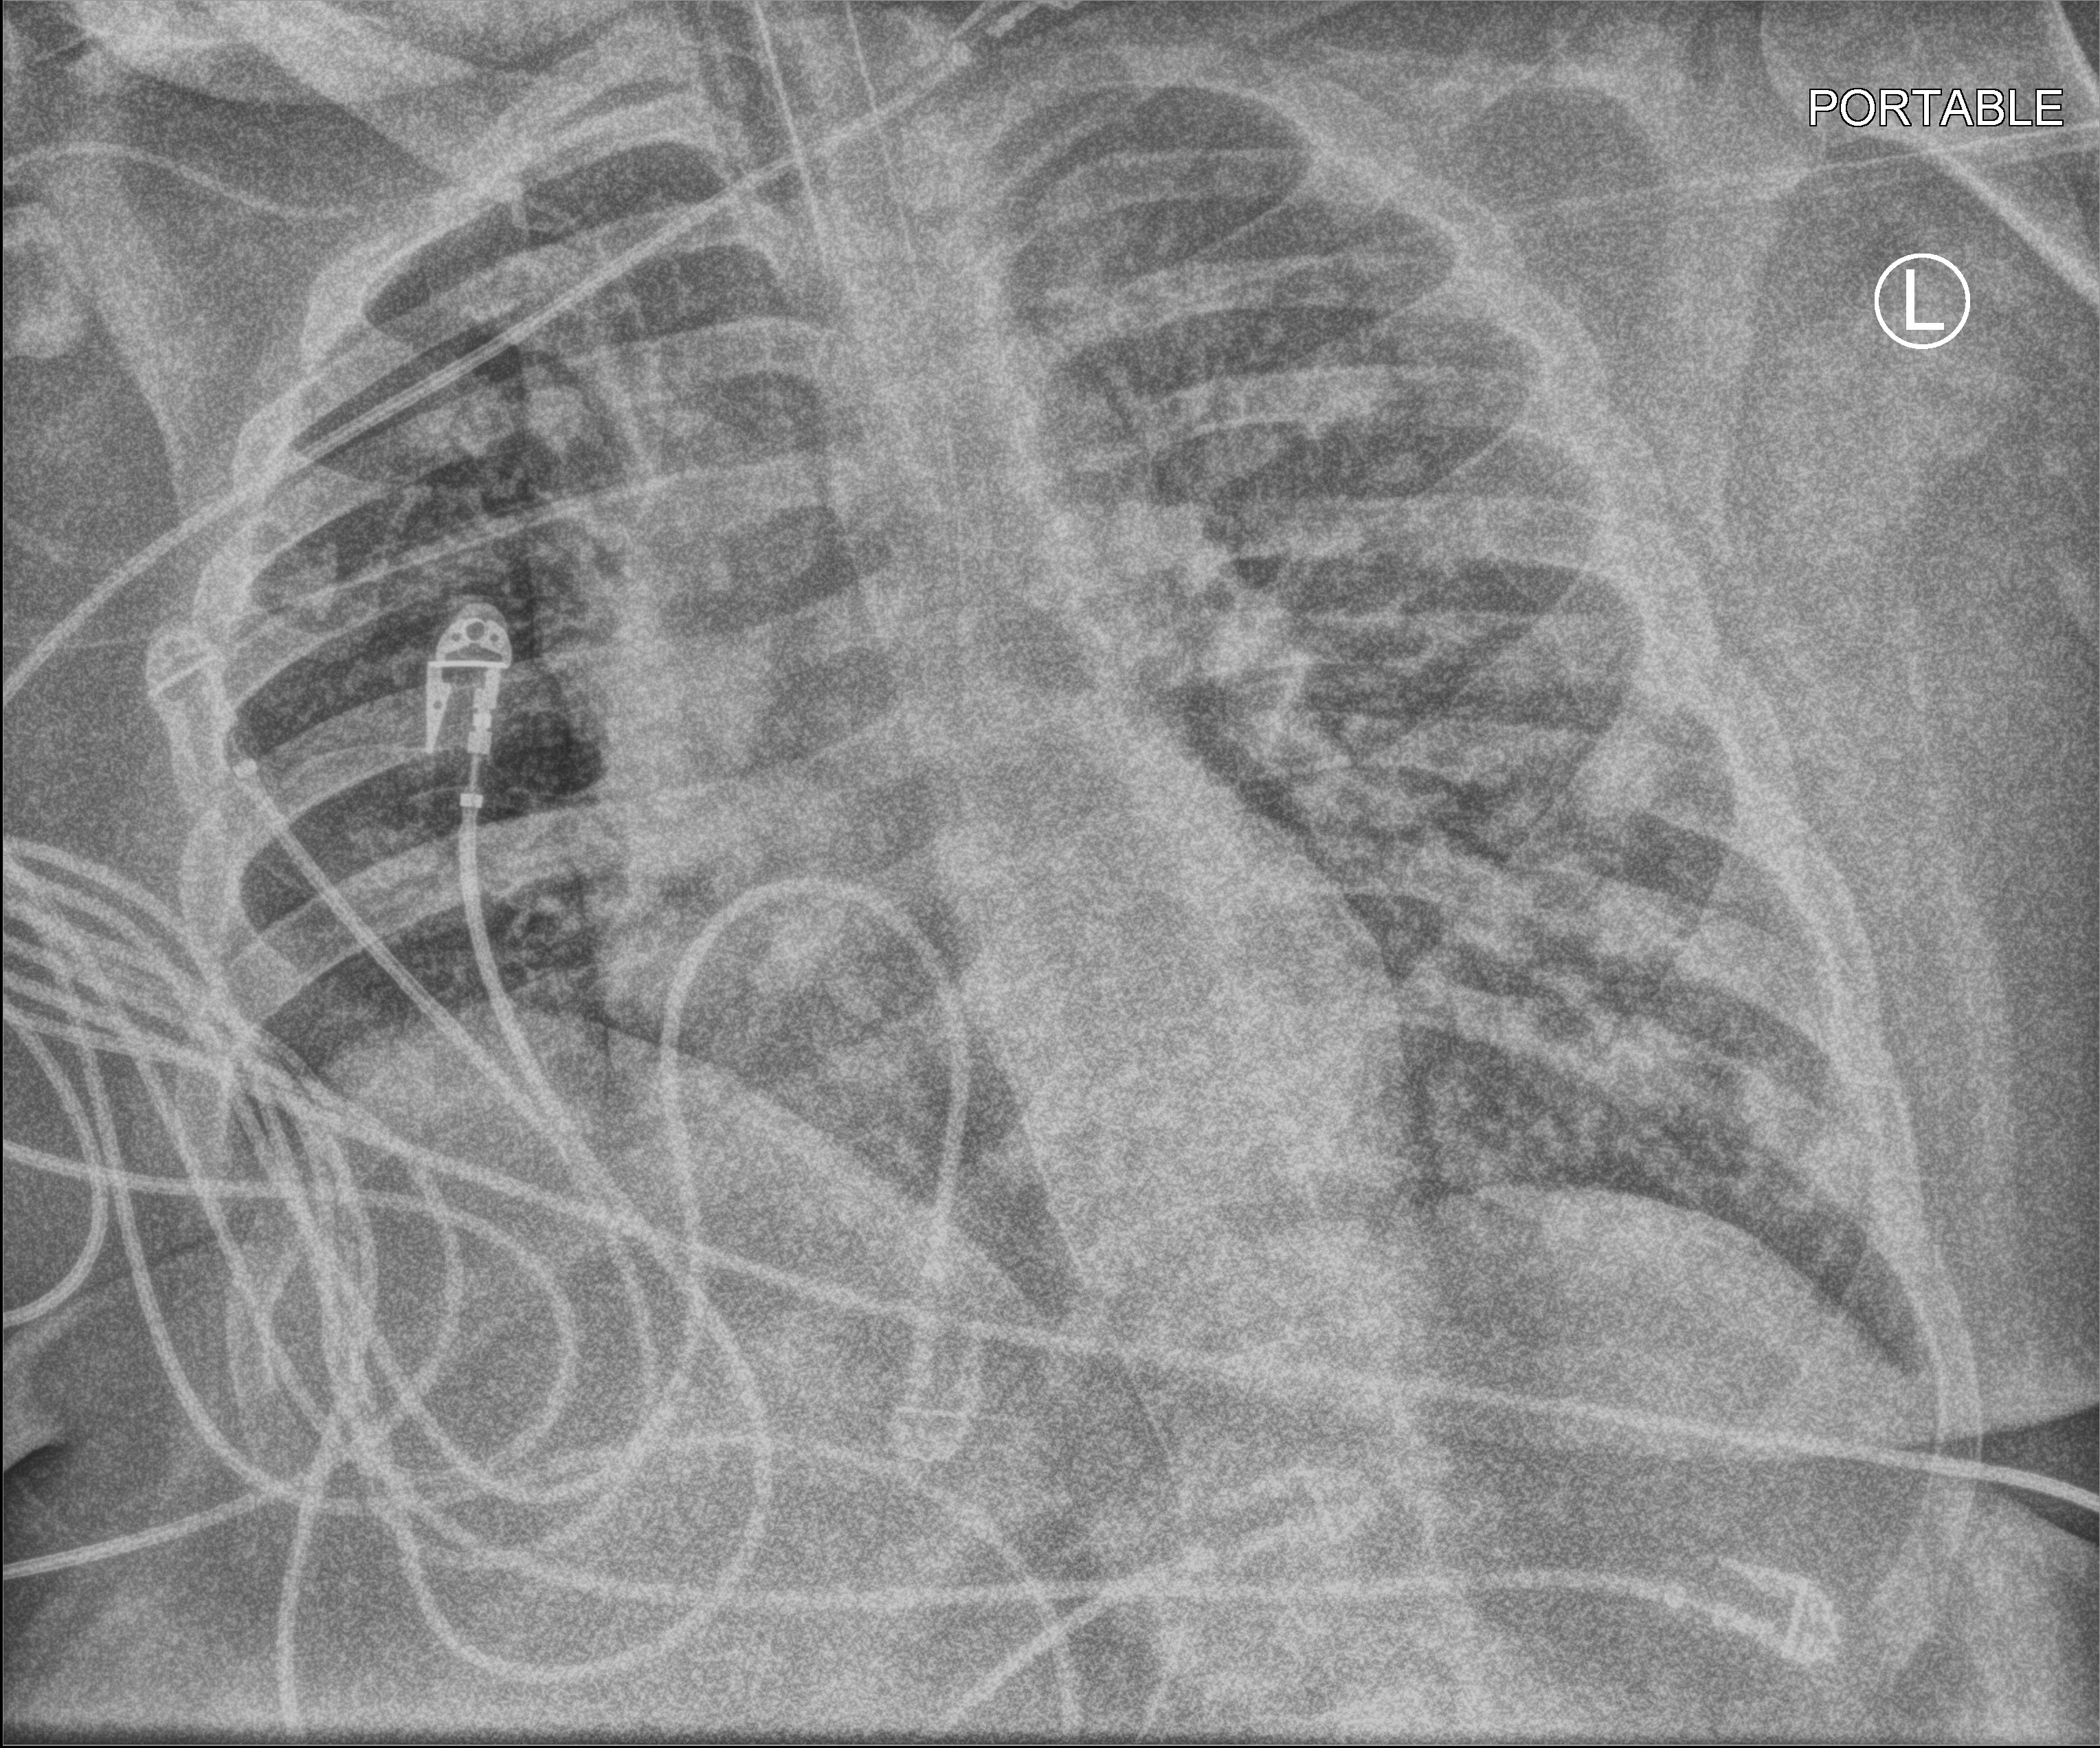
Bedside chest radiograph (computed radiography); anteroposterior (AP) projection. Adult patient hospitalised with COVID-19, age 18–59 years.
Hospital-stay facts (about this admission, not read from this image; timing relative to this image not recorded): admitted to intensive care during this hospital stay: yes; mechanically ventilated during this hospital stay: yes; hypertension (admission record): yes.